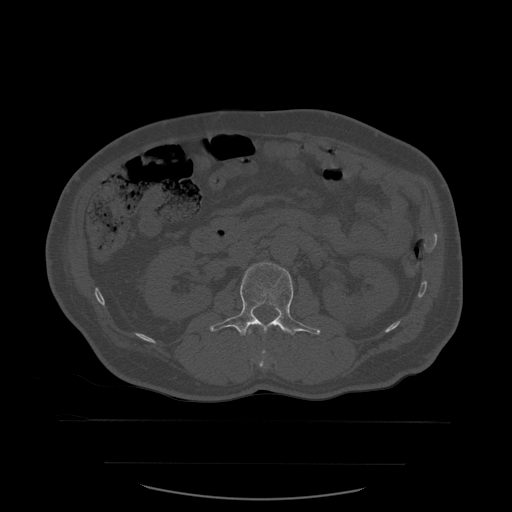
CT including the spine, one axial slice; position 223 of 590 along the scan axis; bone window (W 1800 / L 400 HU); 1.25 mm slice thickness; 512 × 512 image matrix, field of view 479 × 479 mm. Patient age 71 years. Case-level facts recorded for this patient, not image findings: primary cancer: lung; vertebrae with lytic lesions (as recorded): T1, T2, L5, S1.
Annotated regions visible in this slice (semi-automatically segmented with operator editing):
- L1 vertebra: bounding box [x1, y1, x2, y2] px = [249, 332, 266, 369]
- L2 vertebra: [210, 263, 321, 336]